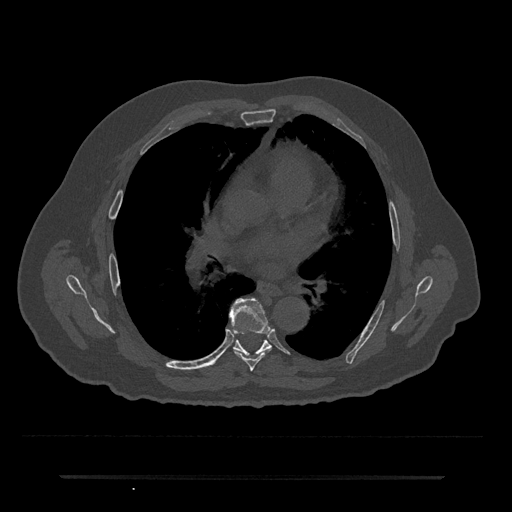
CT including the spine, one axial slice; slice 415 of 797 in the series (ordered by position); reconstruction kernel Br40s/3; 120 kVp; bone window (W 1800 / L 400 HU); 0.5 mm slice thickness; 512 × 512 image matrix, field of view 437 × 437 mm. Patient: male, 69 years. Case-level facts recorded for this patient, not image findings: primary cancer: prostate.
Annotated regions visible in this slice (semi-automatically segmented with operator editing):
- T6 vertebra: bounding box (x1, y1, x2, y2) in pixels: (230, 298, 273, 371)
- T7 vertebra: (233, 340, 271, 356)